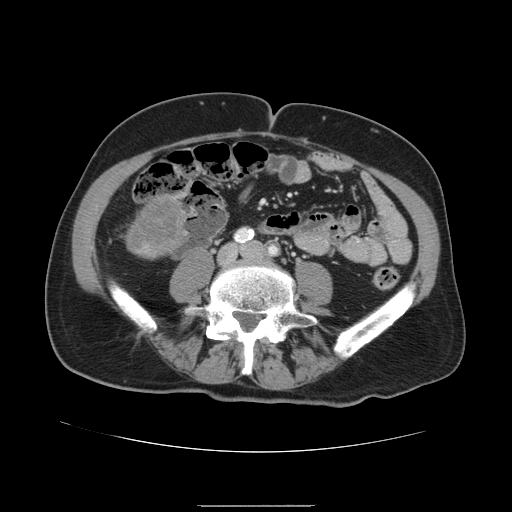
Contrast-enhanced abdominal CT, one axial slice; 120 kVp; intravenous contrast given; soft-tissue window (W 400 / L 40 HU); 2.5 mm slice thickness; 512 × 512 image matrix, field of view 386 × 386 mm. Male patient, age 74 years. From the clinical record (not read from this slice): diagnosis: colorectal cancer liver metastases, imaged before liver resection.
Outlined on this slice (outlined manually by an expert reader):
- liver: bounding box <126,194,189,261> (left, top, right, bottom; pixels)
- liver metastasis: <128,198,183,254>